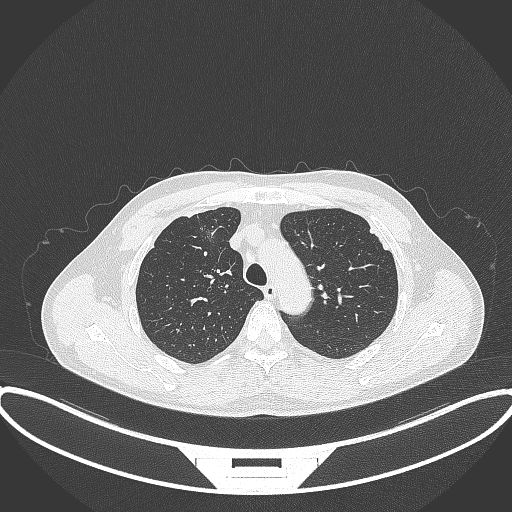
Chest CT, one axial slice. Position 273 of 395 along the scan axis. Reconstruction kernel B70f. 120 kVp. Lung window (W 1500 / L -600 HU). 512 × 512 image matrix, field of view 424 × 424 mm. Male patient, age 60 years. From the clinical record (not read from this slice): clinical TNM (as recorded): T1c N0 M0.
Structures marked on this image (rectangle marked by the reading radiologist):
- lung tumour (recorded histology: adenocarcinoma): bounding box <194,213,225,256> (left, top, right, bottom; pixels)